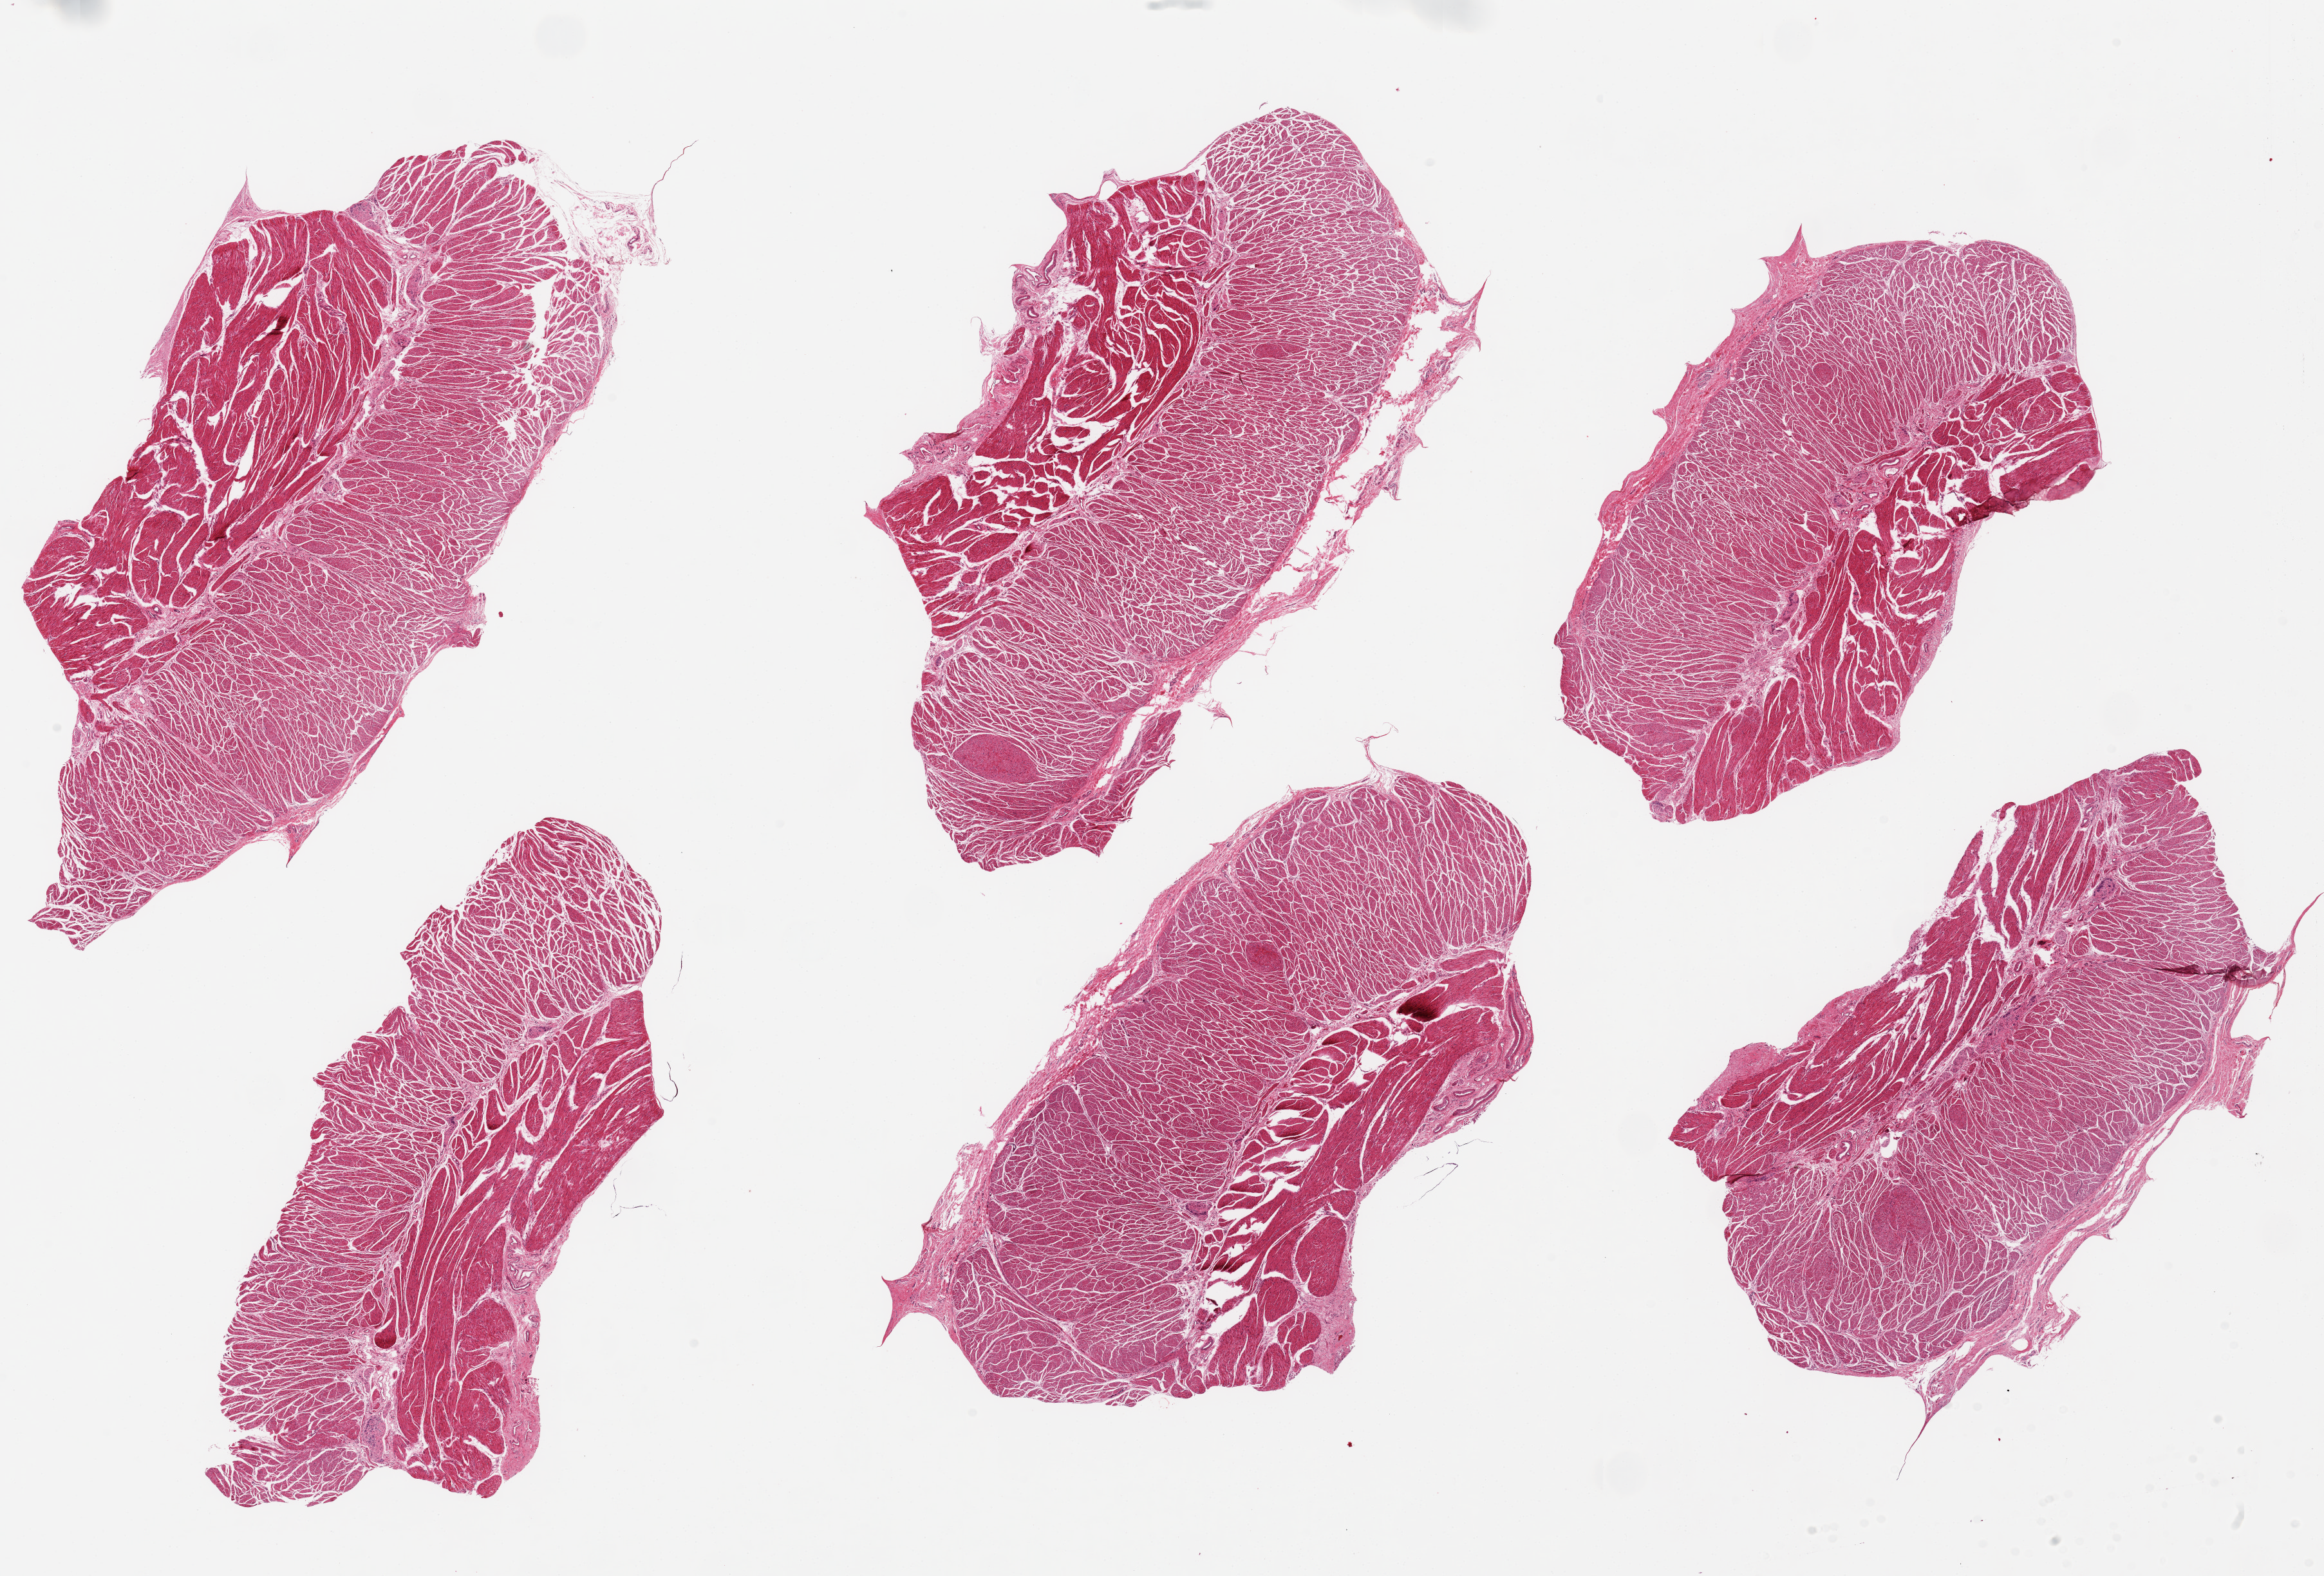
H&E whole-slide image, a low-resolution overview of the entire scanned area, about 28.5 x 19.4 mm (from a 20x scan); PAXgene-fixed paraffin-embedded (PFPE) section; section of esophageal muscle (target tissue); donor tissue sample. Female donor.
• reviewer comment on this tissue sample: 6 pieces, up to 11x5mm; good clean specimens